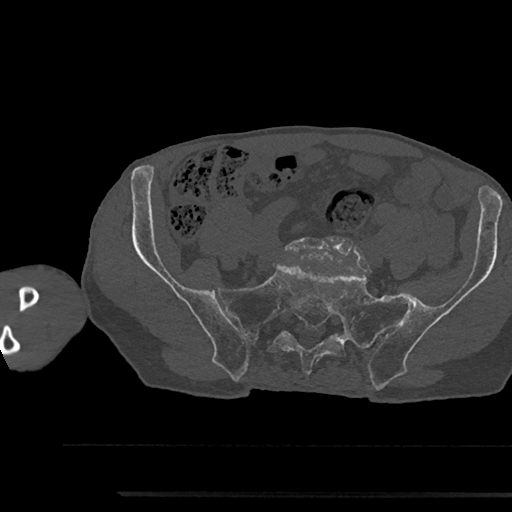
CT including the spine, one axial slice. Position 289 of 797 along the scan axis. Reconstruction kernel Br40s/3. 120 kVp. Bone window (W 1800 / L 400 HU). 0.5 mm slice thickness. 512 × 512 image matrix, field of view 367 × 367 mm. Patient: male, 79 years. Case-level facts recorded for this patient, not image findings: primary cancer: prostate.
Annotated regions visible in this slice (semi-automatically segmented with operator editing):
- L5 vertebra: bounding box (x1, y1, x2, y2) in pixels: (284, 238, 364, 268)